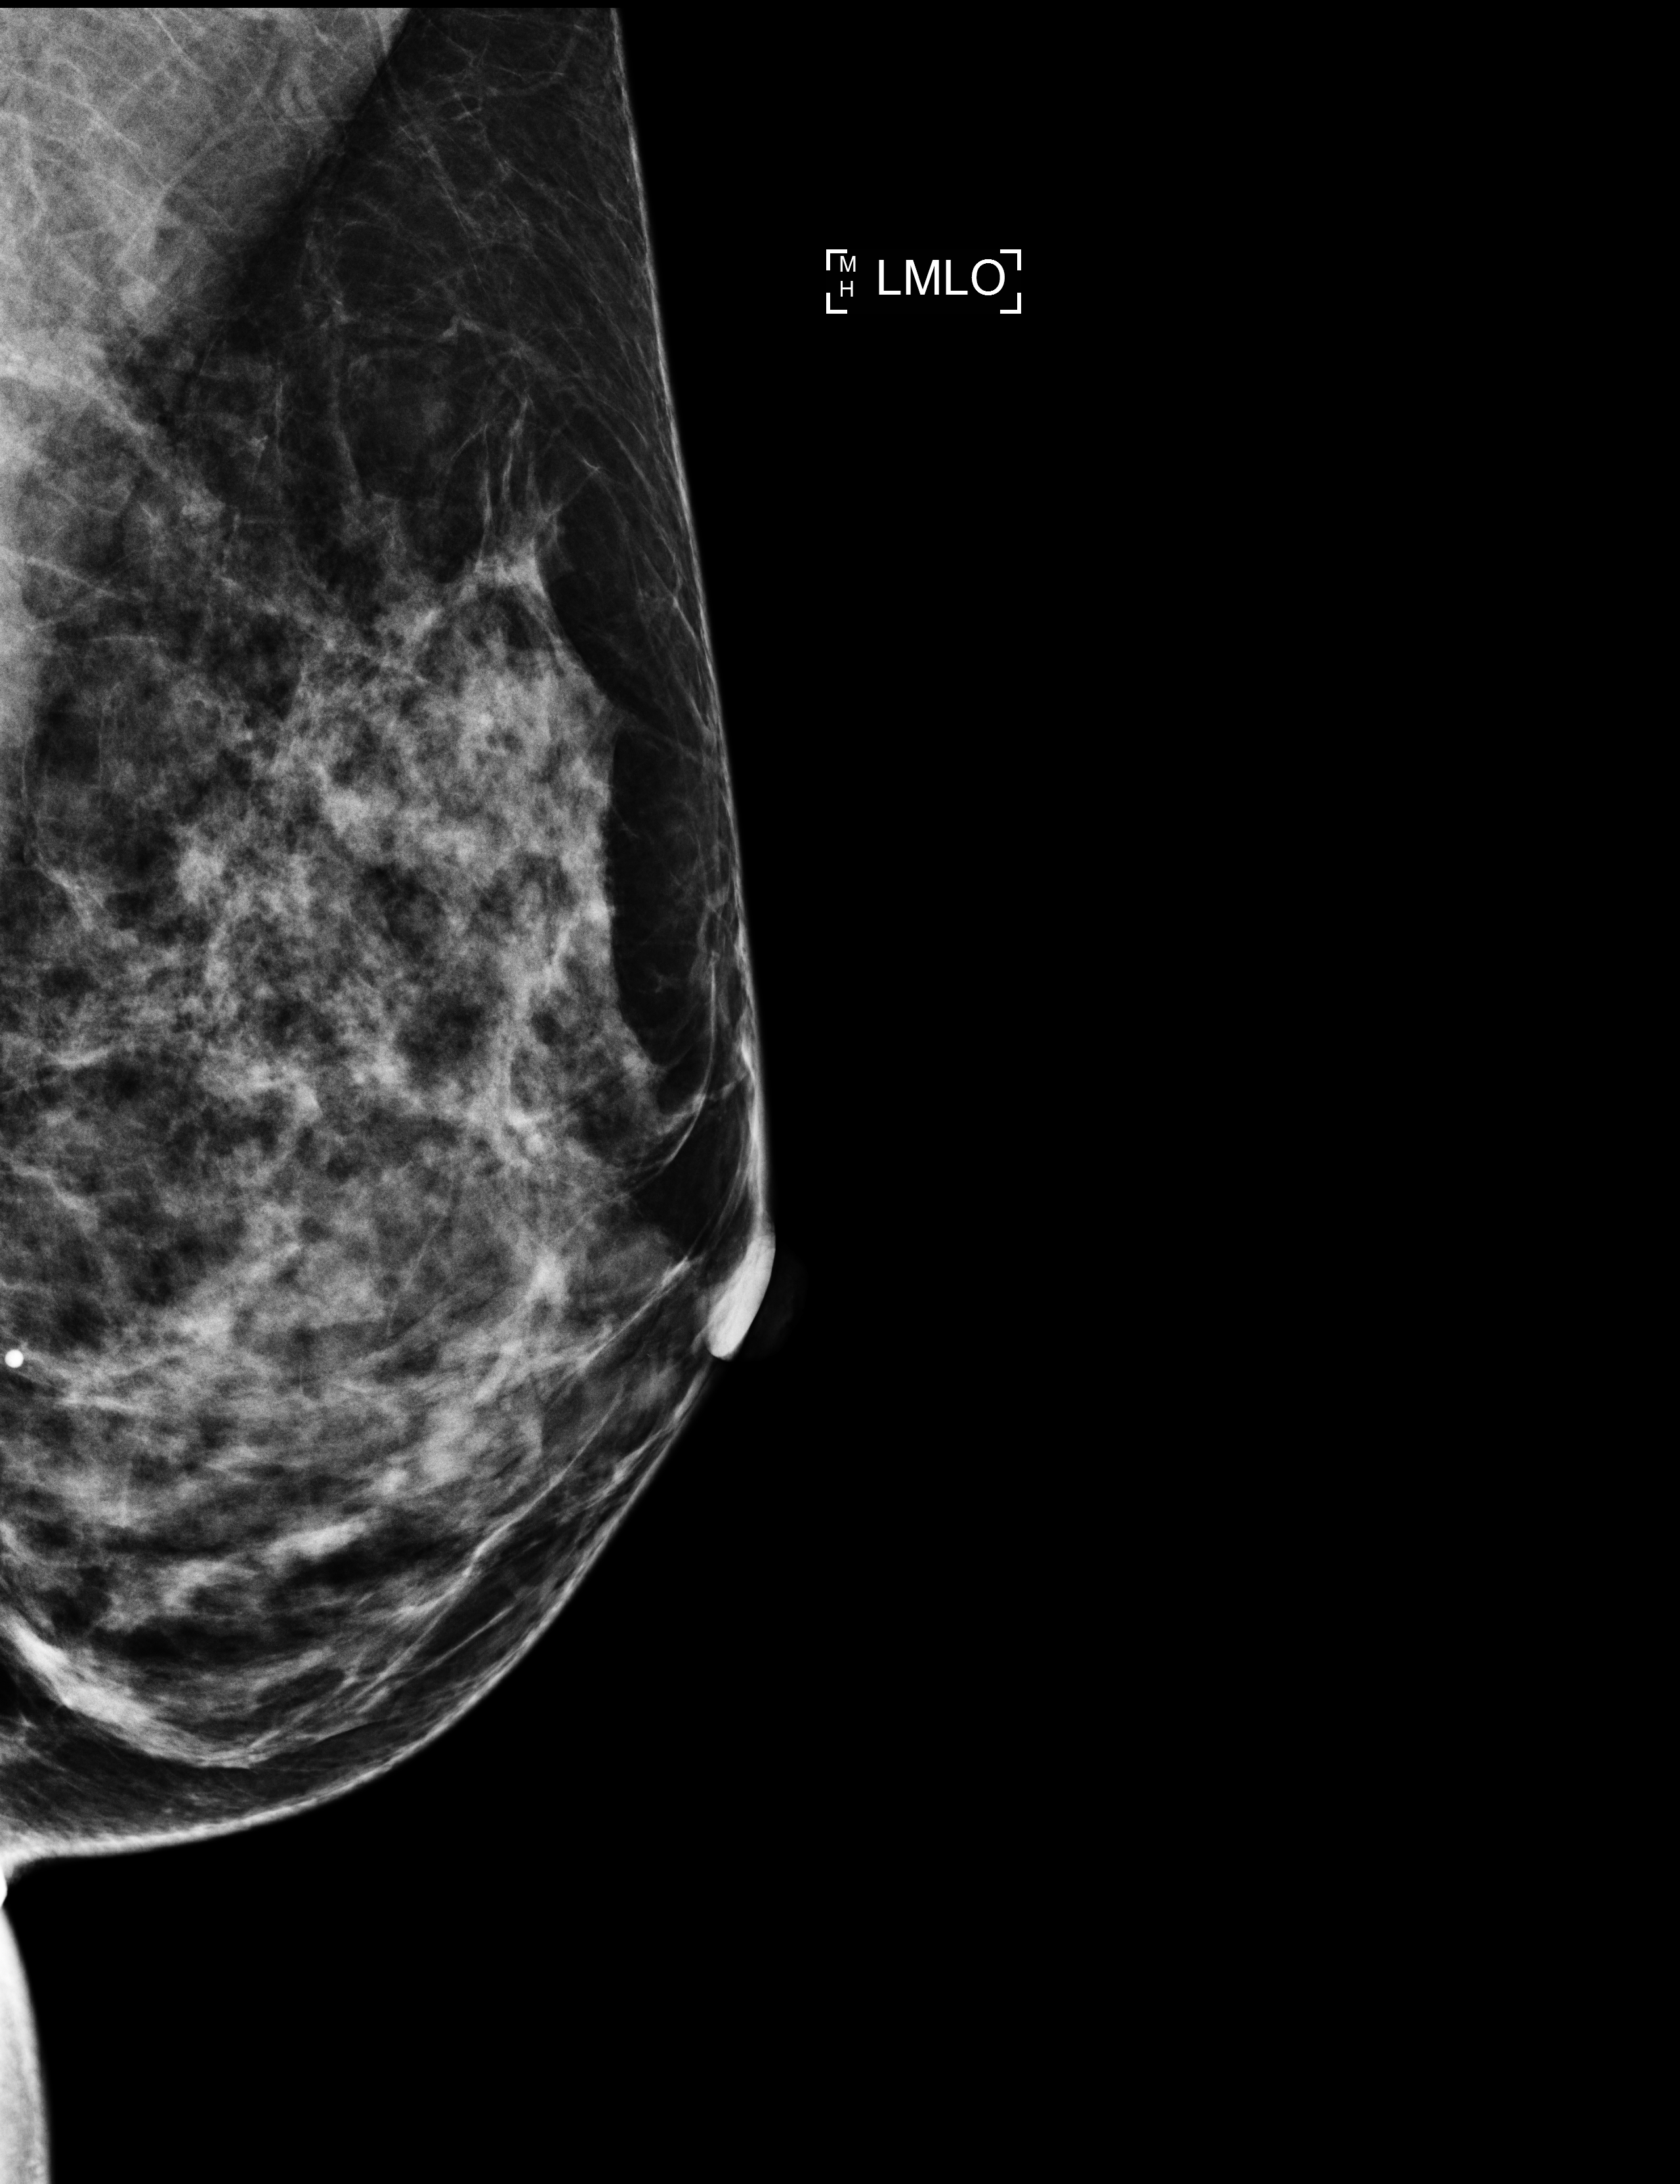
Full-field digital mammogram (FFDM), left breast, MLO view, annual screening mammography examination, compressed breast thickness 55 mm, system: Selenia Dimensions. Female patient, age 41 years.
BI-RADS breast density category at the screening exam (both breasts, scale 1–4): 4. Final BI-RADS category for the screening round (tomosynthesis exam, both breasts): category 1. Recall: no recall after this screen.